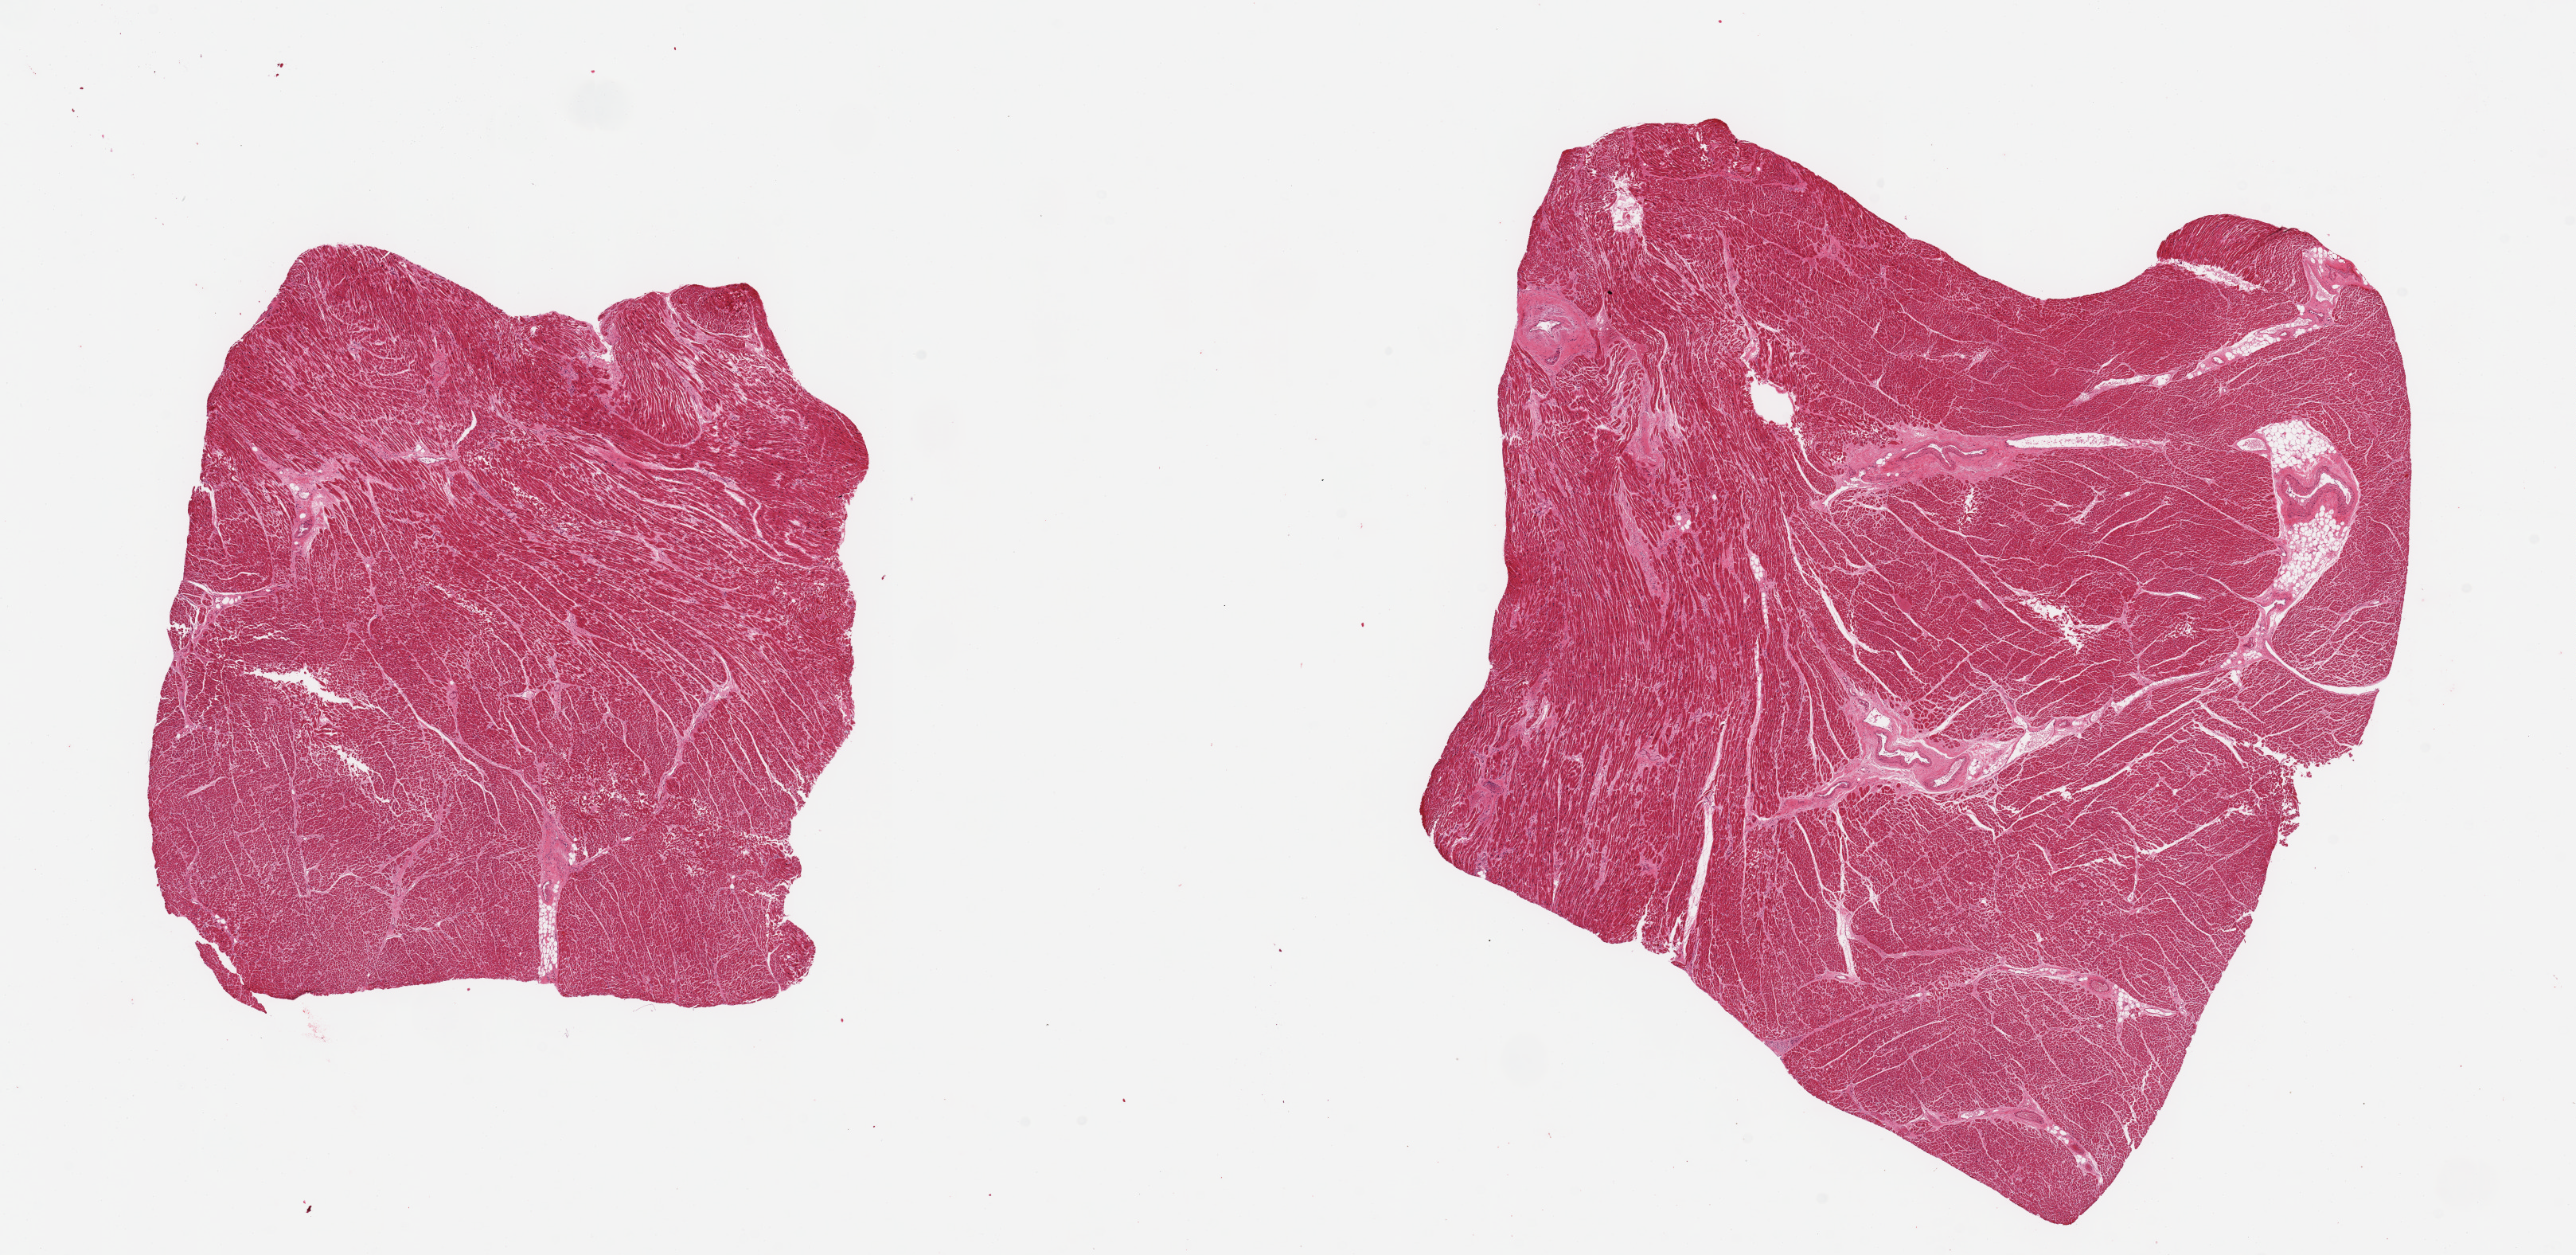
Whole-slide image, haematoxylin and eosin stain, brightfield, whole scanned area (about 25.6 x 12.5 mm, from a 20x scan) shown as a low-resolution overview; PAXgene-fixed, paraffin-embedded tissue; target tissue: heart; donor tissue sample. Male donor.
Review note (as recorded): 2 pieces; enlarged fibers and nuclei; focal interstitial fibrosis.